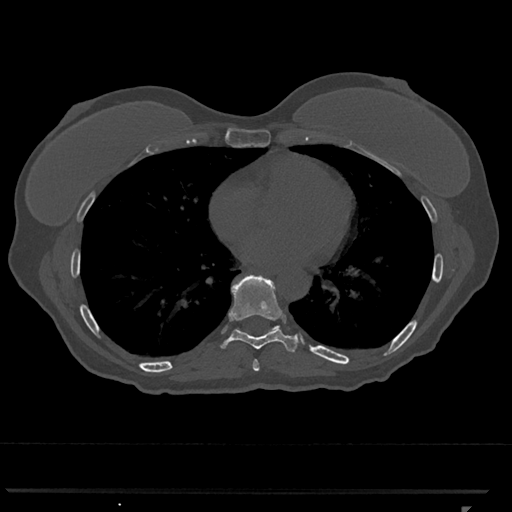
CT including the spine, one axial slice. Position 660 of 793 along the scan axis. Reconstruction kernel Br40s/3. 120 kVp. Bone window (W 1800 / L 400 HU). 0.5 mm slice thickness. 512 × 512 image matrix. Female patient, age 62 years. From the clinical record (not read from this slice): primary cancer: renal.
Annotated regions visible in this slice (semi-automatic segmentation, software-assisted and operator-edited):
- T7 vertebra: bounding box <253,359,260,371> (left, top, right, bottom; pixels)
- T8 vertebra: <222,275,299,352>
- T9 vertebra: <237,325,281,330>